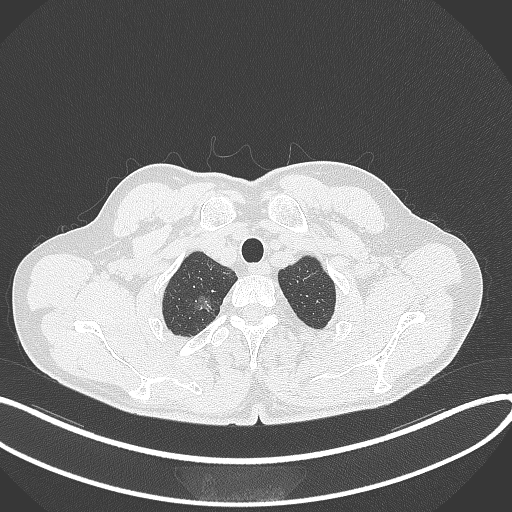
Chest CT, one axial slice. Position 352 of 407 along the scan axis. Lung window (W 1500 / L -600 HU). 512 × 512 image matrix. Male patient, age 58 years. Case-level facts recorded for this patient, not image findings: clinical TNM (as recorded): T1c N0 M0; histopathological grade: G1-2.
Structures marked on this image (bounding box drawn by a radiologist):
- lung tumour (recorded histology: adenocarcinoma): bounding box <191,289,214,318> (left, top, right, bottom; pixels)